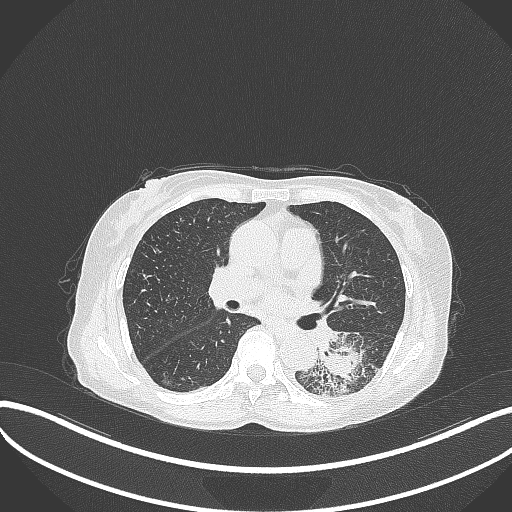
Chest CT, one axial slice; position 173 of 370 along the scan axis; reconstruction kernel B70f; lung window (W 1500 / L -600 HU); 1 mm slice thickness; 512 × 512 image matrix, field of view 400 × 400 mm. Female patient, age 78 years. Case-level facts recorded for this patient, not image findings: clinical TNM (as recorded): T3 N0 M1.
Annotated regions visible in this slice (rectangle marked by the reading radiologist):
- lung tumour (recorded histology: squamous cell carcinoma): bounding box [x1, y1, x2, y2] px = [312, 325, 386, 399]